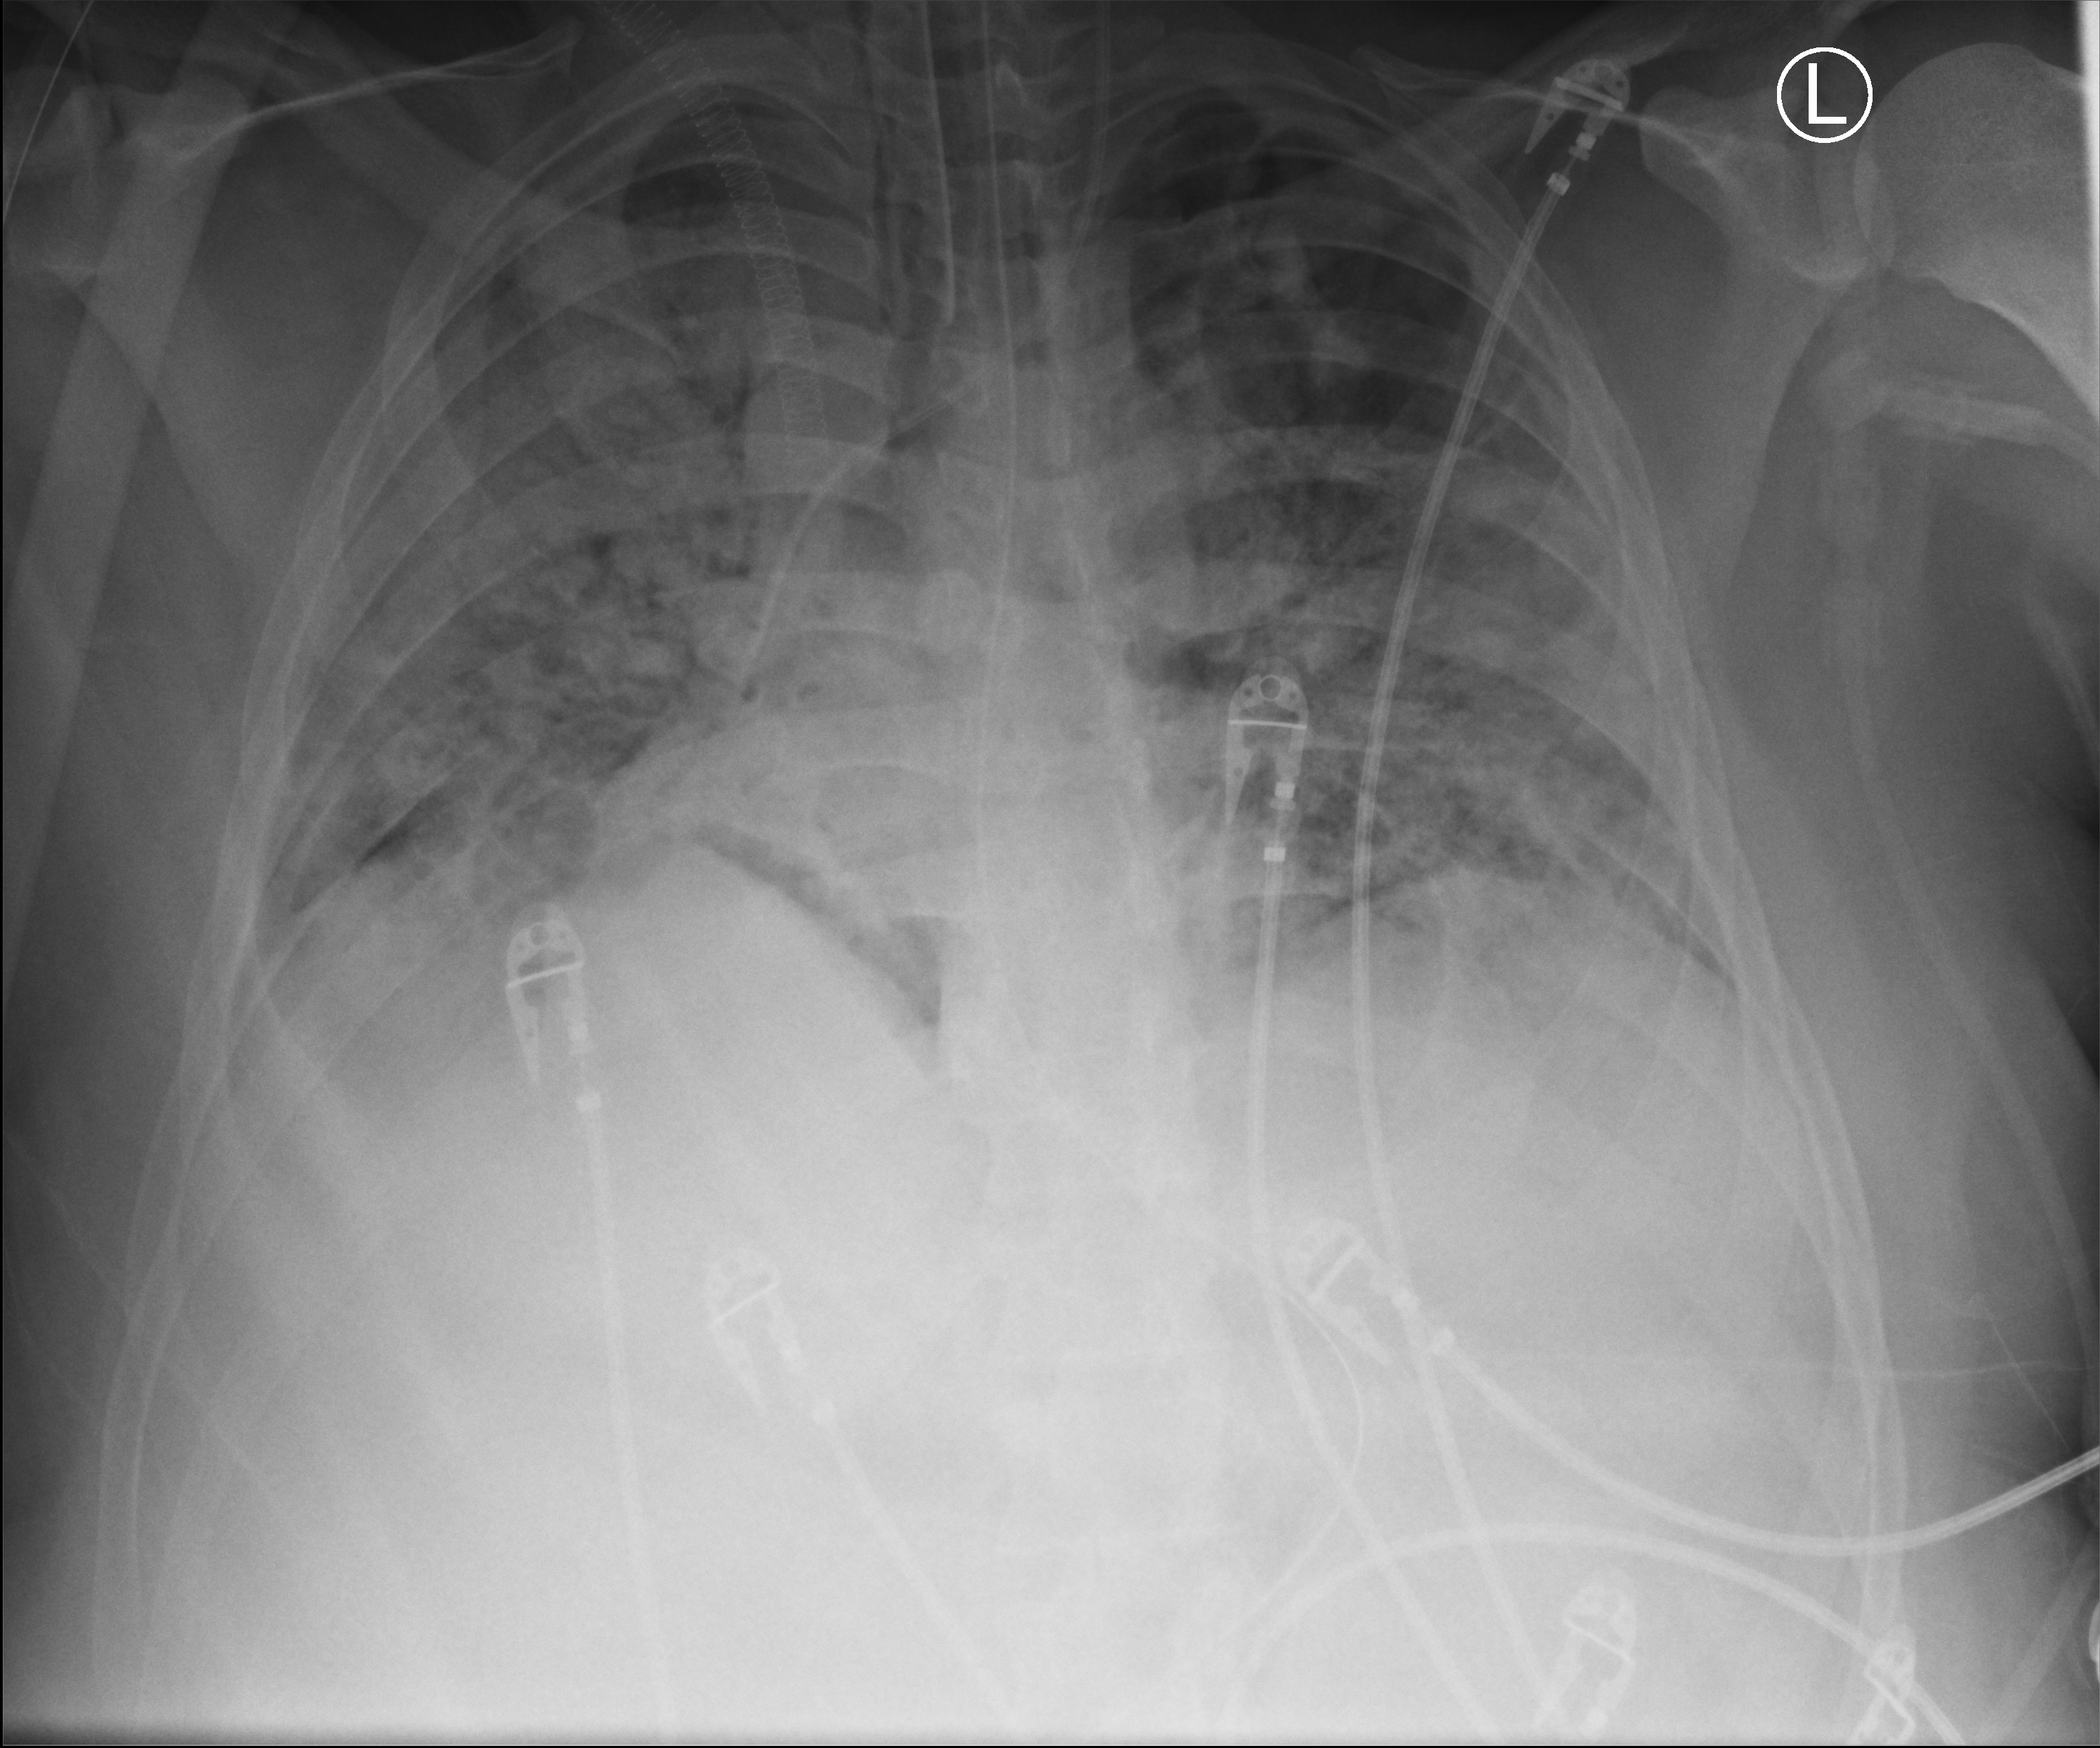
Bedside chest radiograph (computed radiography), anteroposterior (AP) projection. Patient hospitalised with COVID-19, aged 18–59 years.
From the hospital-stay record, not from the radiograph (when in the stay this image was taken is not recorded):
- other chronic lung disease (admission record): no
- admitted to intensive care during this hospital stay: yes